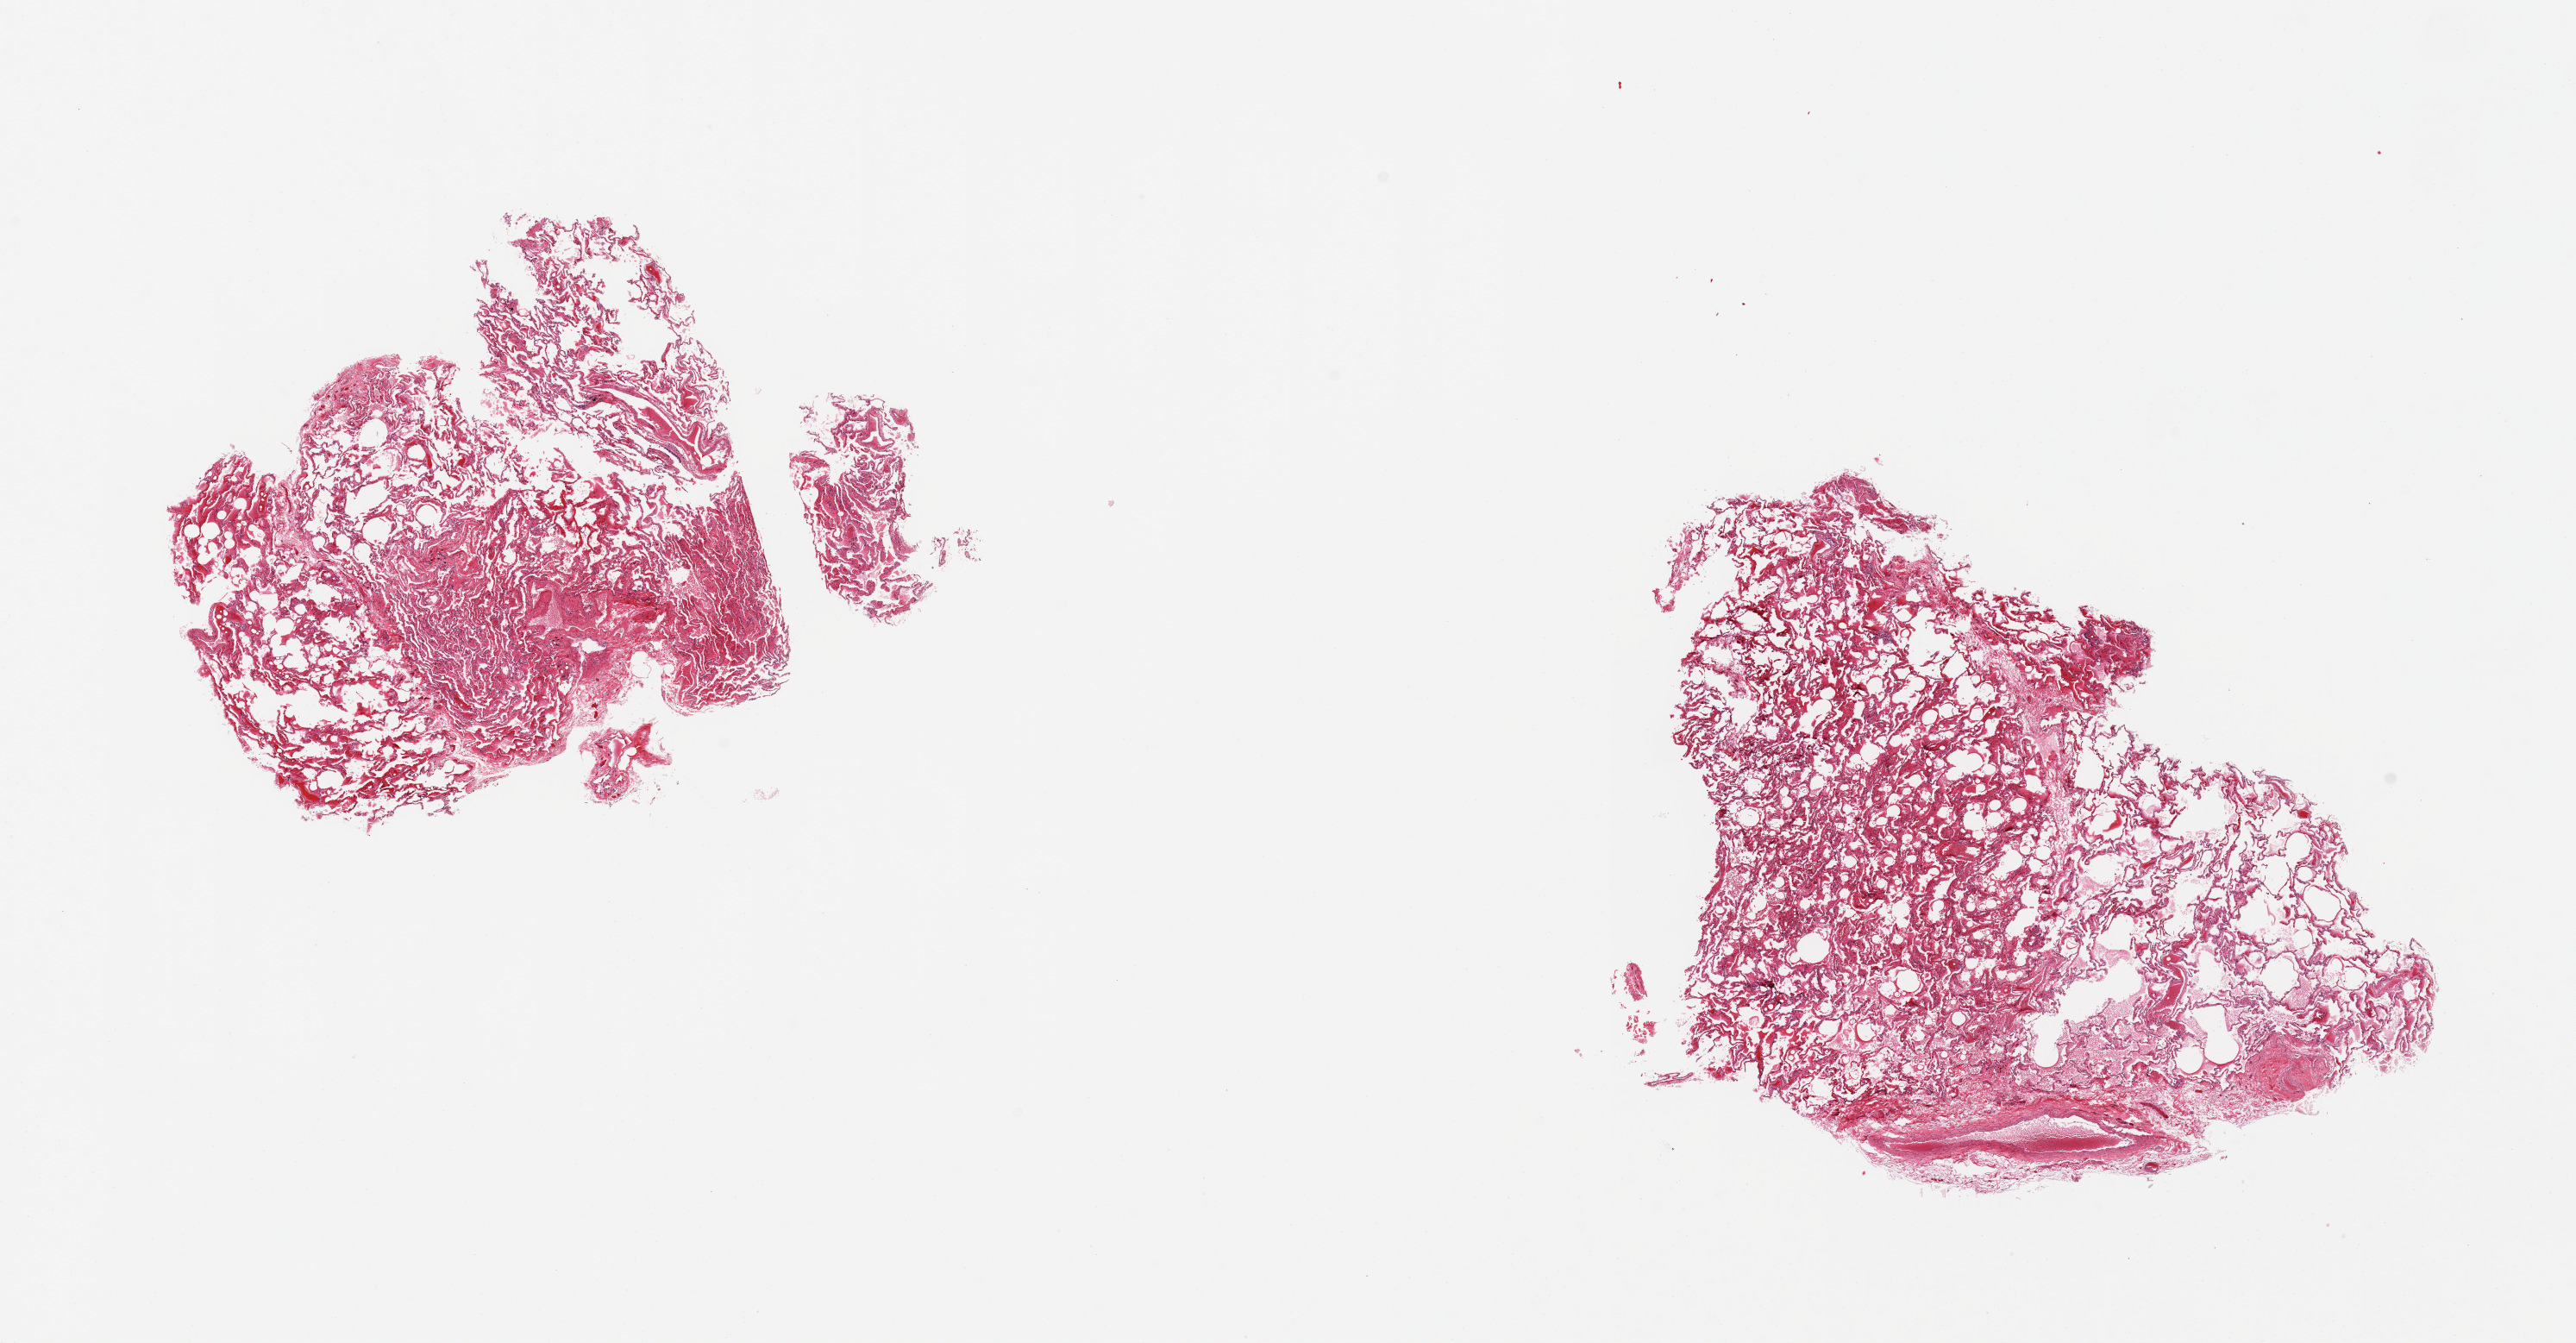
Digitized H&E-stained section — shown as a low-resolution overview of the whole scanned area (about 23.6 x 12.3 mm, from a 20x scan). PAXgene-fixed paraffin-embedded (PFPE) section. Section of lung (target tissue). Donor tissue sample. Male donor.
• reviewer comment on this tissue sample: 2 pieces; patchy moderate vascular congestion; foci of emphysema